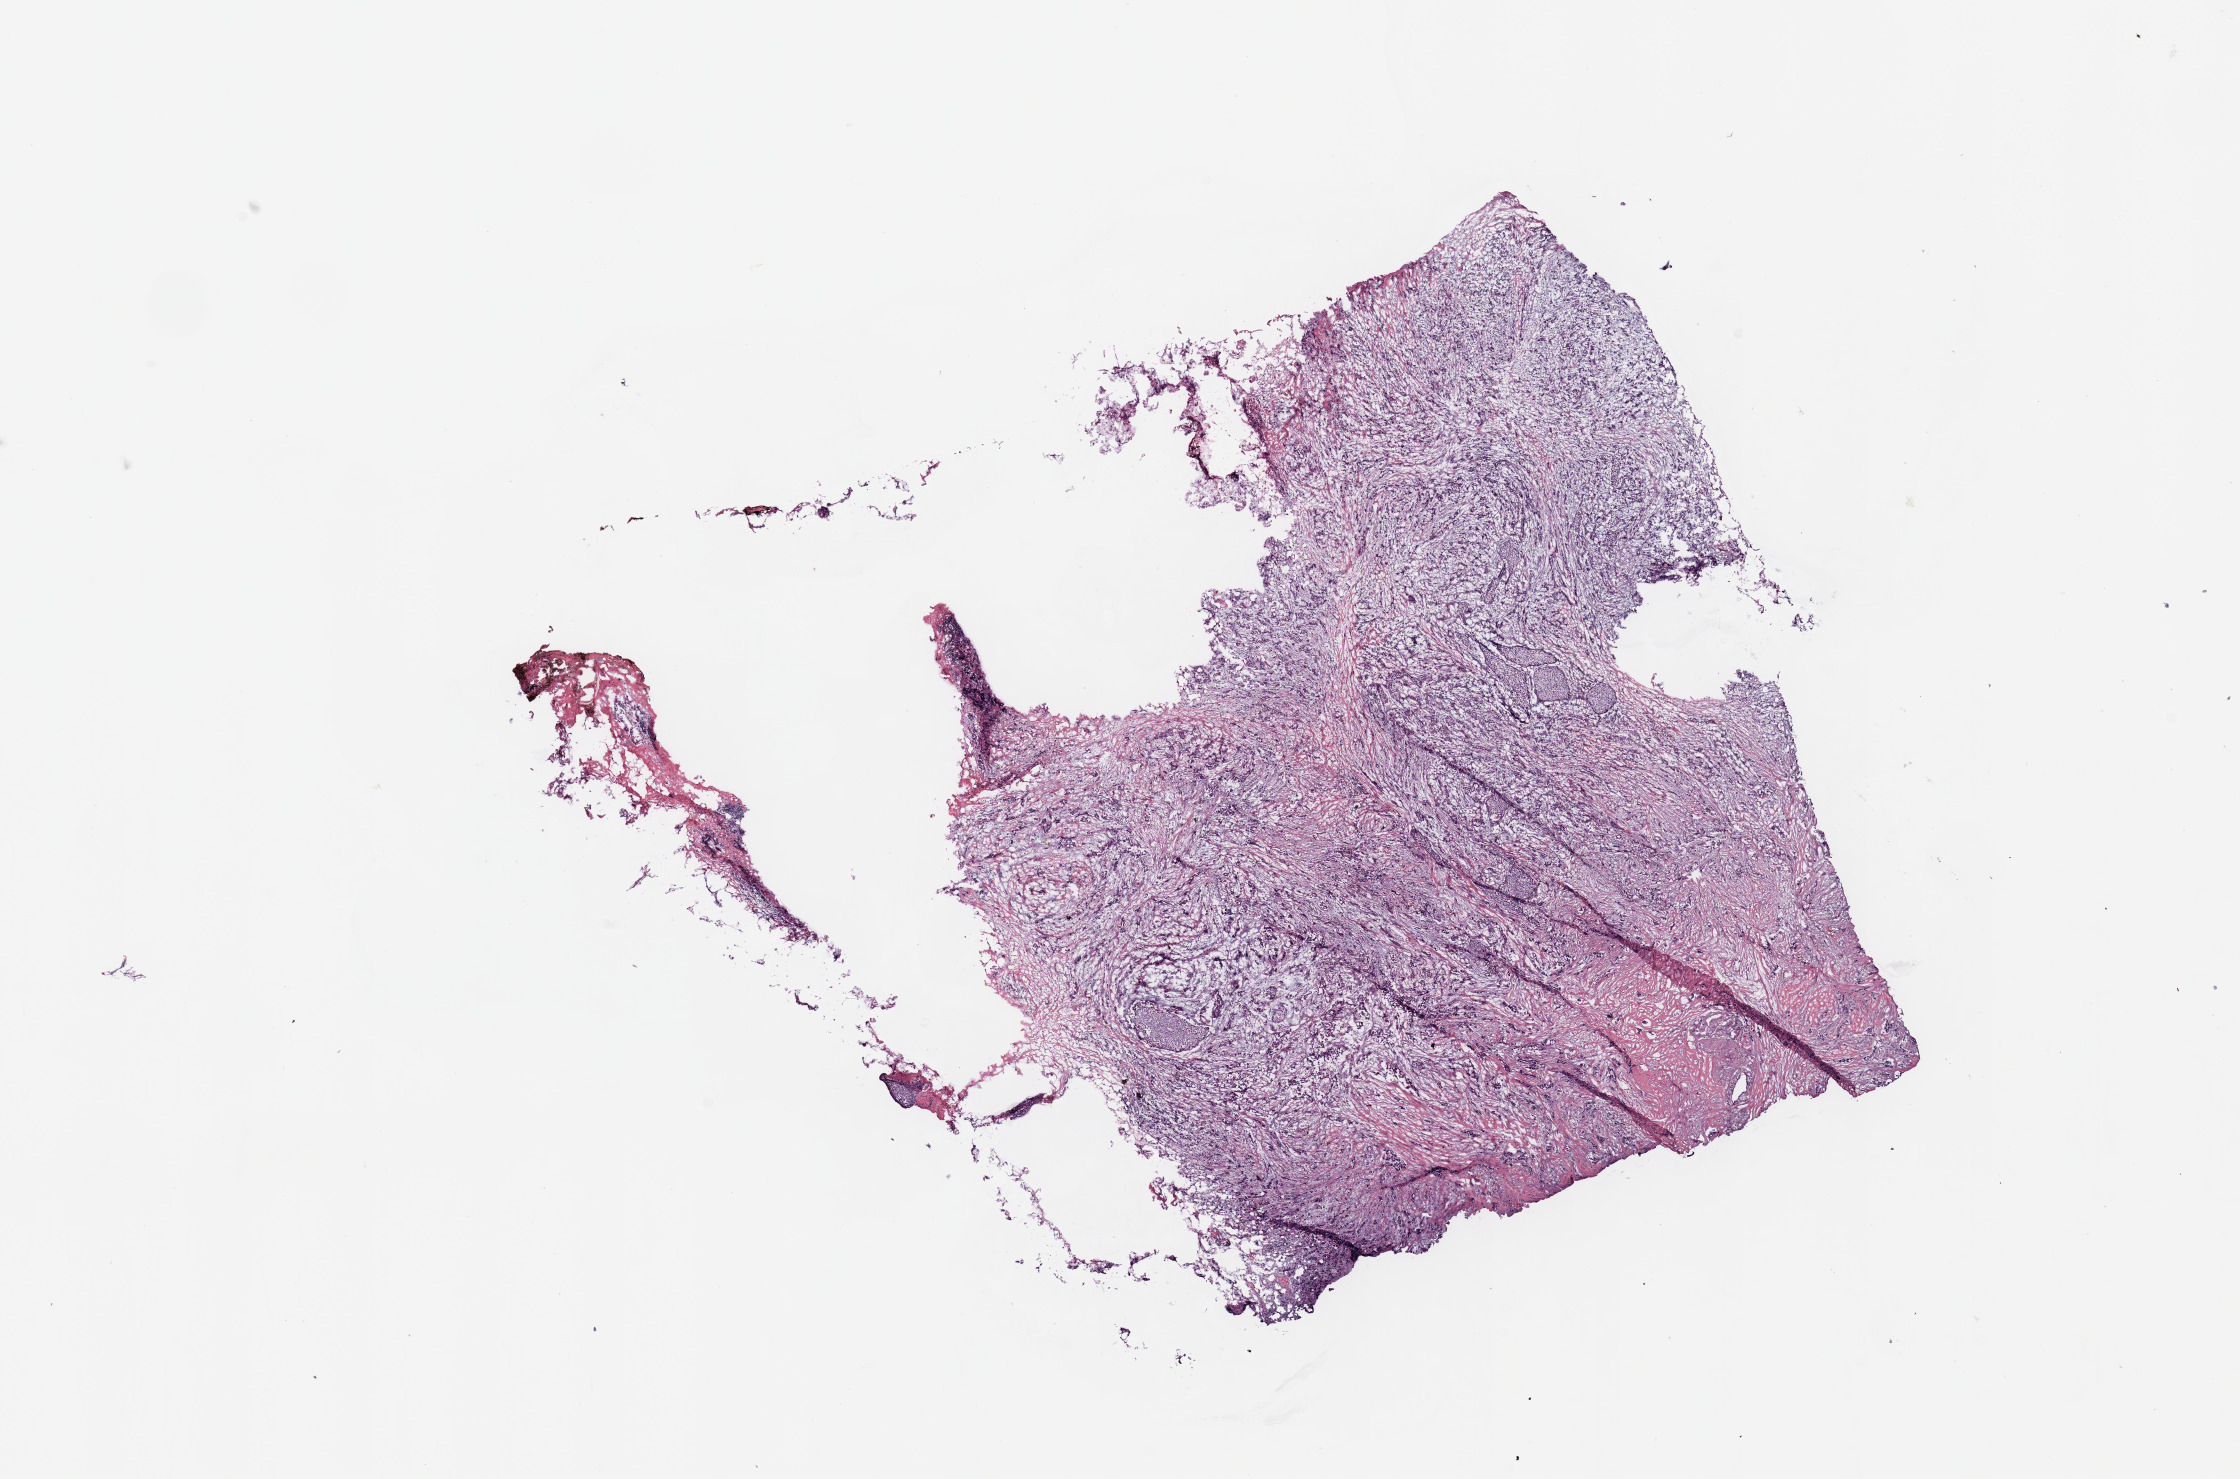
H&E-stained whole-slide image — whole scanned area (about 17.7 x 11.7 mm) shown as a low-resolution overview. Breast, tissue type not recorded.
- patient diagnosis (cohort enrolment): breast cancer (breast)